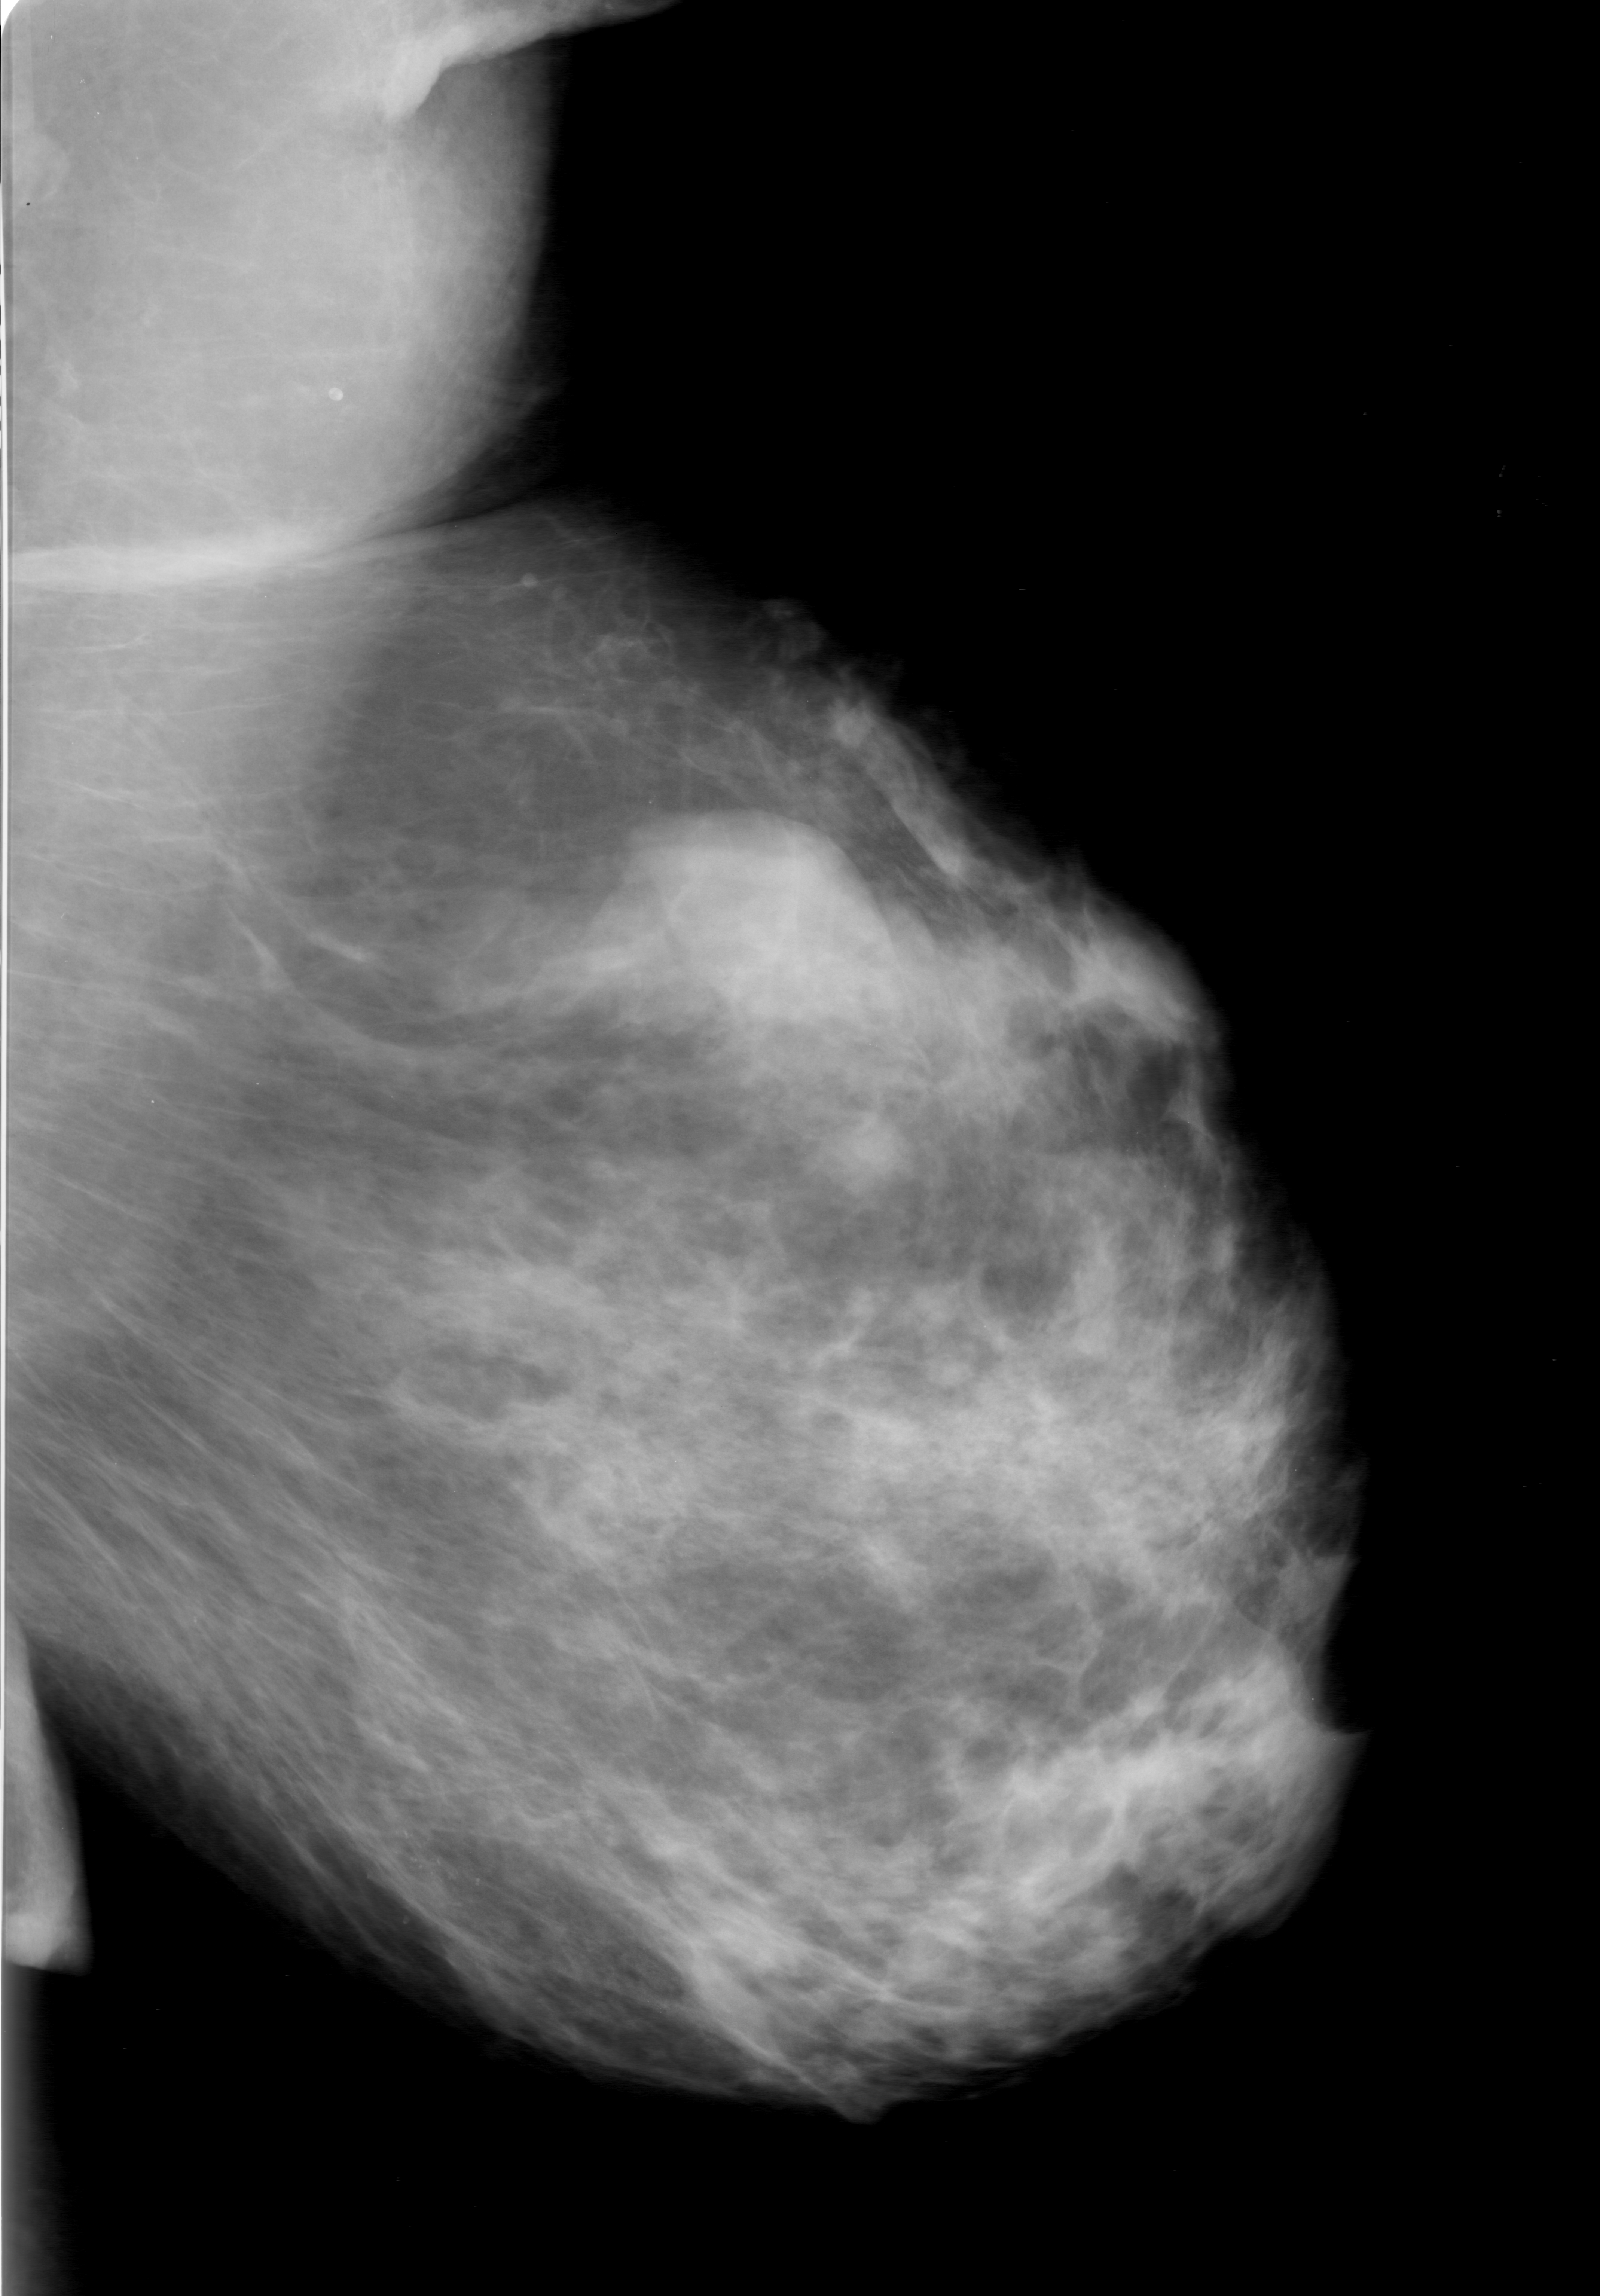
Scanned film-screen mammogram; left breast; mediolateral oblique (MLO) view.
Calcifications, morphology punctate / fine linear branching, distribution clustered; BI-RADS assessment category 0 (incomplete: needs additional imaging); pathology (as recorded): malignant.